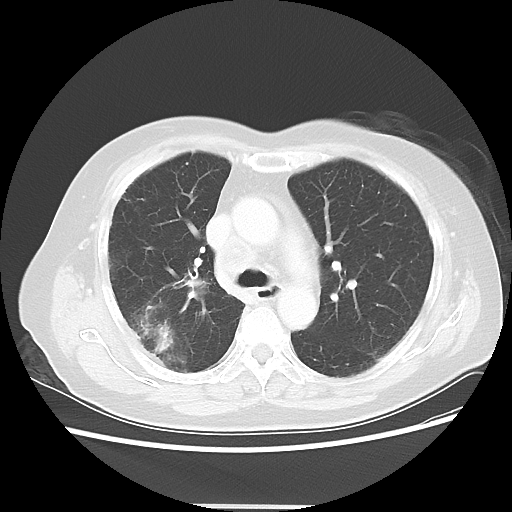
Chest CT, one axial slice. Position 32 of 50 along the scan axis. Reconstruction kernel LUNG. 120 kVp. Lung window (W 1500 / L -600 HU). 5 mm slice thickness. 512 × 512 image matrix, field of view 360 × 360 mm. Patient: female, 72 years. From the clinical record (not read from this slice): clinical TNM (as recorded): T2 N1 M0.
Structures marked on this image (bounding box drawn by a radiologist):
- lung tumour (recorded histology: adenocarcinoma): bounding box [x1, y1, x2, y2] px = [152, 316, 176, 357]